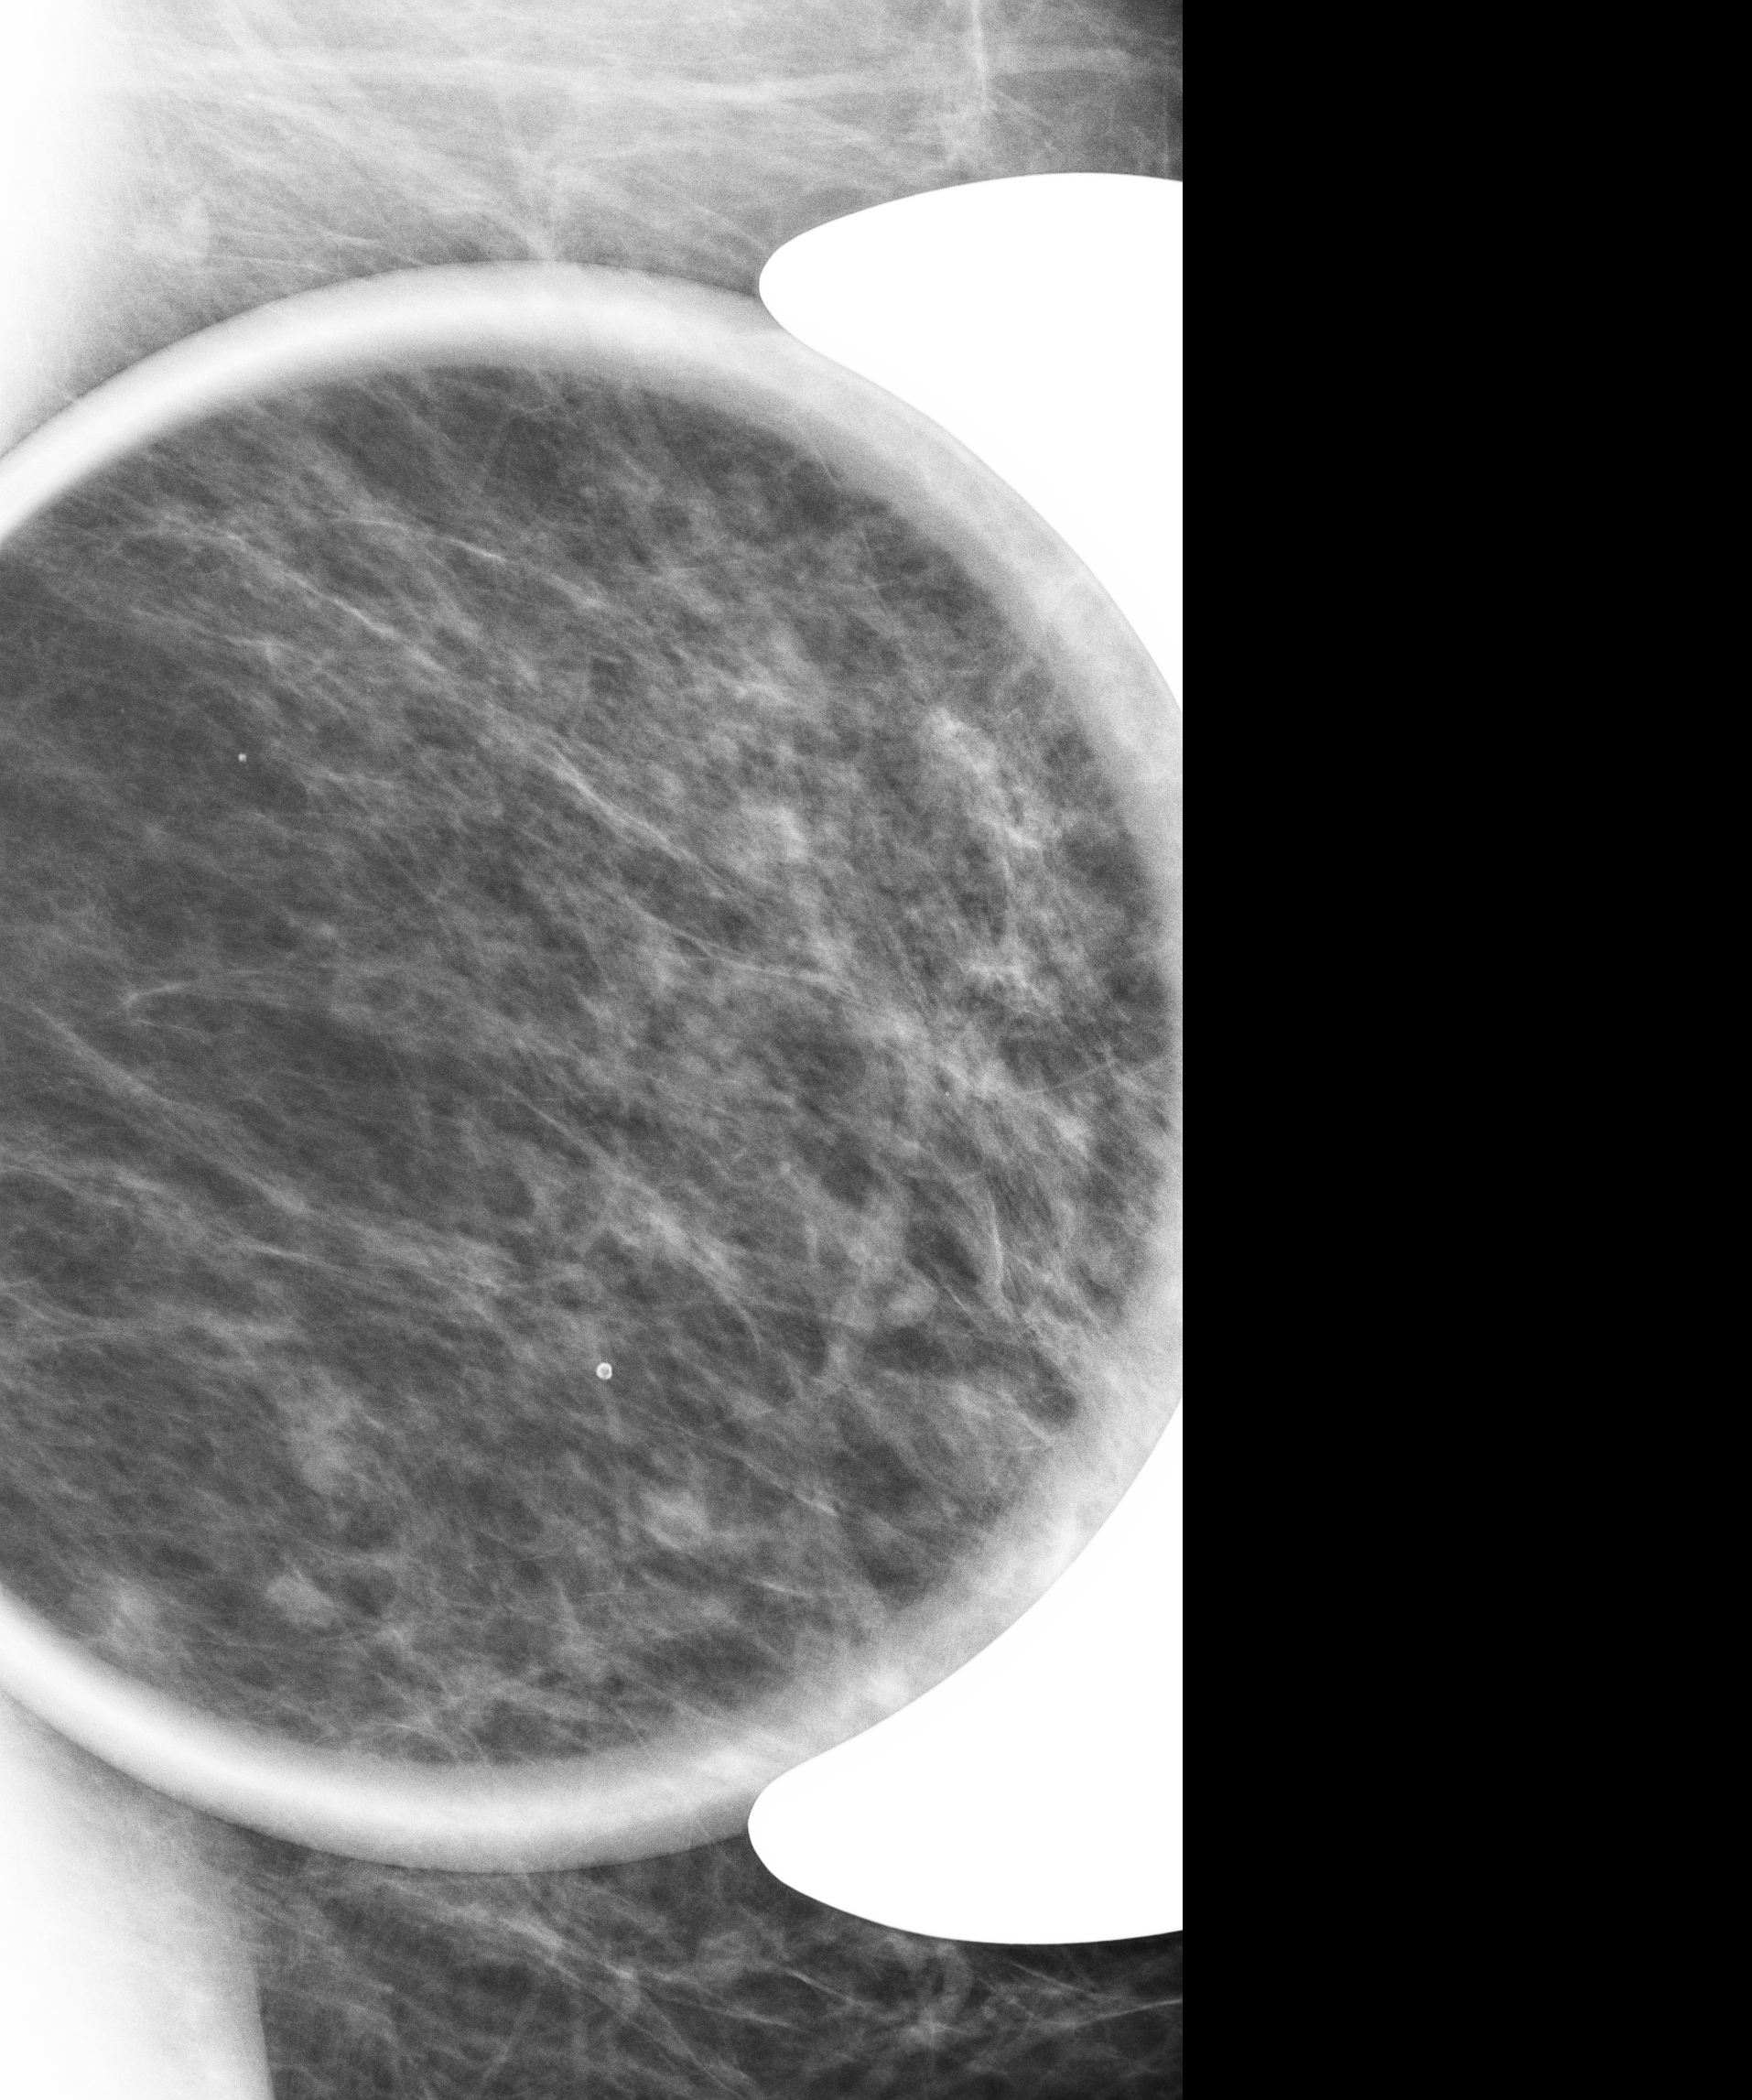
Digital mammogram (FFDM); left breast; mediolateral (ML) view; diagnostic work-up study; system: Senographe Essential ADS_56.21.3. Patient aged 53 years (female).
- breast density at the screening exam (both breasts): heterogeneously dense (BI-RADS density category c)
- final BI-RADS assessment for this screening round (tomosynthesis exam, both breasts): category 4
- recall: recalled for additional imaging after this screen